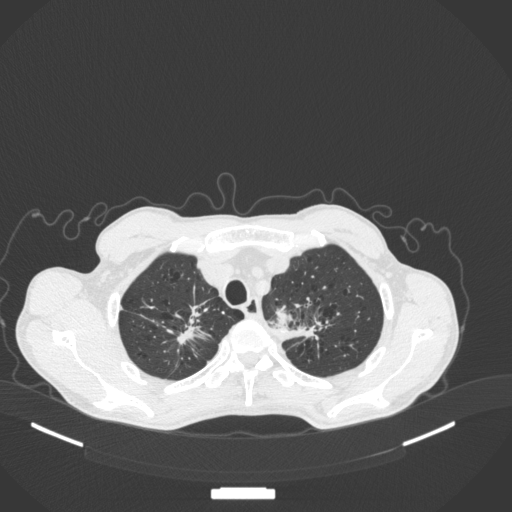
Chest CT, one axial slice. Position 365 of 394 along the scan axis. 120 kVp. Lung window (W 1500 / L -600 HU). 512 × 512 image matrix, field of view 400 × 400 mm. Patient: male, 65 years. Case-level facts recorded for this patient, not image findings: clinical TNM (as recorded): T2b N0 M0; histopathological grade: G2.
Structures marked on this image (rectangle marked by the reading radiologist):
- lung tumour (recorded histology: adenocarcinoma): bounding box <270,303,294,330> (left, top, right, bottom; pixels)